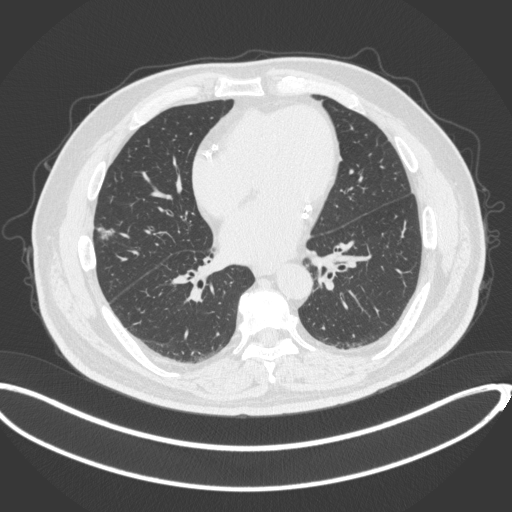
Chest CT, one axial slice. Position 141 of 342 along the scan axis. Lung window (W 1500 / L -600 HU). 1 mm slice thickness. 512 × 512 image matrix, field of view 427 × 427 mm. Male patient, age 68 years. From the clinical record (not read from this slice): clinical TNM (as recorded): T1c N0 M0; histopathological grade: G2.
Annotated regions visible in this slice (rectangle marked by the reading radiologist):
- lung tumour (recorded histology: adenocarcinoma): bounding box (x1, y1, x2, y2) in pixels: (95, 223, 115, 245)